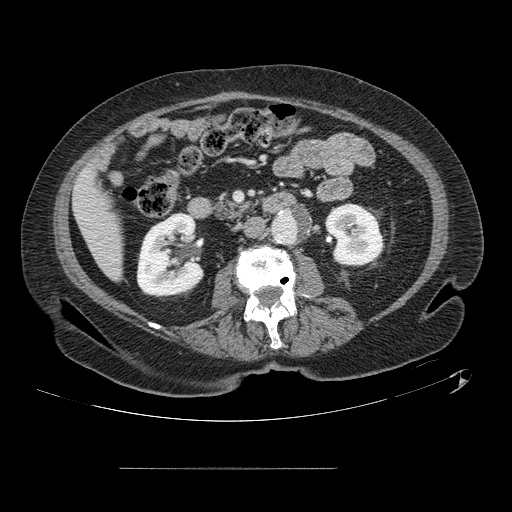
Contrast-enhanced abdominal CT, one axial slice. Position 30 of 148 along the scan axis. 120 kVp. Intravenous contrast given. Soft-tissue window (W 400 / L 40 HU). 512 × 512 image matrix. Female patient, age 75 years. Case-level facts recorded for this patient, not image findings: diagnosis: colorectal cancer liver metastases, imaged before liver resection; multiple liver metastases: no; largest metastasis: 2.4 cm.
Outlined on this slice (expert manual segmentation):
- liver: bounding box [x1, y1, x2, y2] px = [74, 169, 122, 279]
- planned liver remnant (the part of the liver to remain after resection): [74, 169, 122, 279]